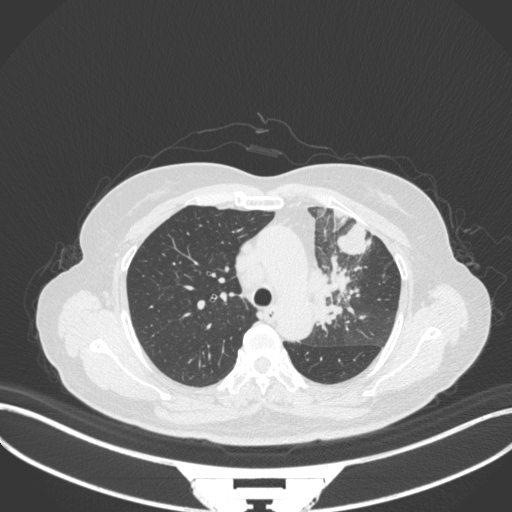
Chest CT, one axial slice; position 239 of 382 along the scan axis; 120 kVp; lung window (W 1500 / L -600 HU); 512 × 512 image matrix, field of view 400 × 400 mm. Patient: female, 64 years. From the clinical record (not read from this slice): clinical TNM (as recorded): T2a N2 M0.
Structures marked on this image (rectangle marked by the reading radiologist):
- lung tumour (recorded histology: adenocarcinoma): bounding box <309,256,358,332> (left, top, right, bottom; pixels)
- lung tumour (recorded histology: adenocarcinoma): <335,217,375,256>